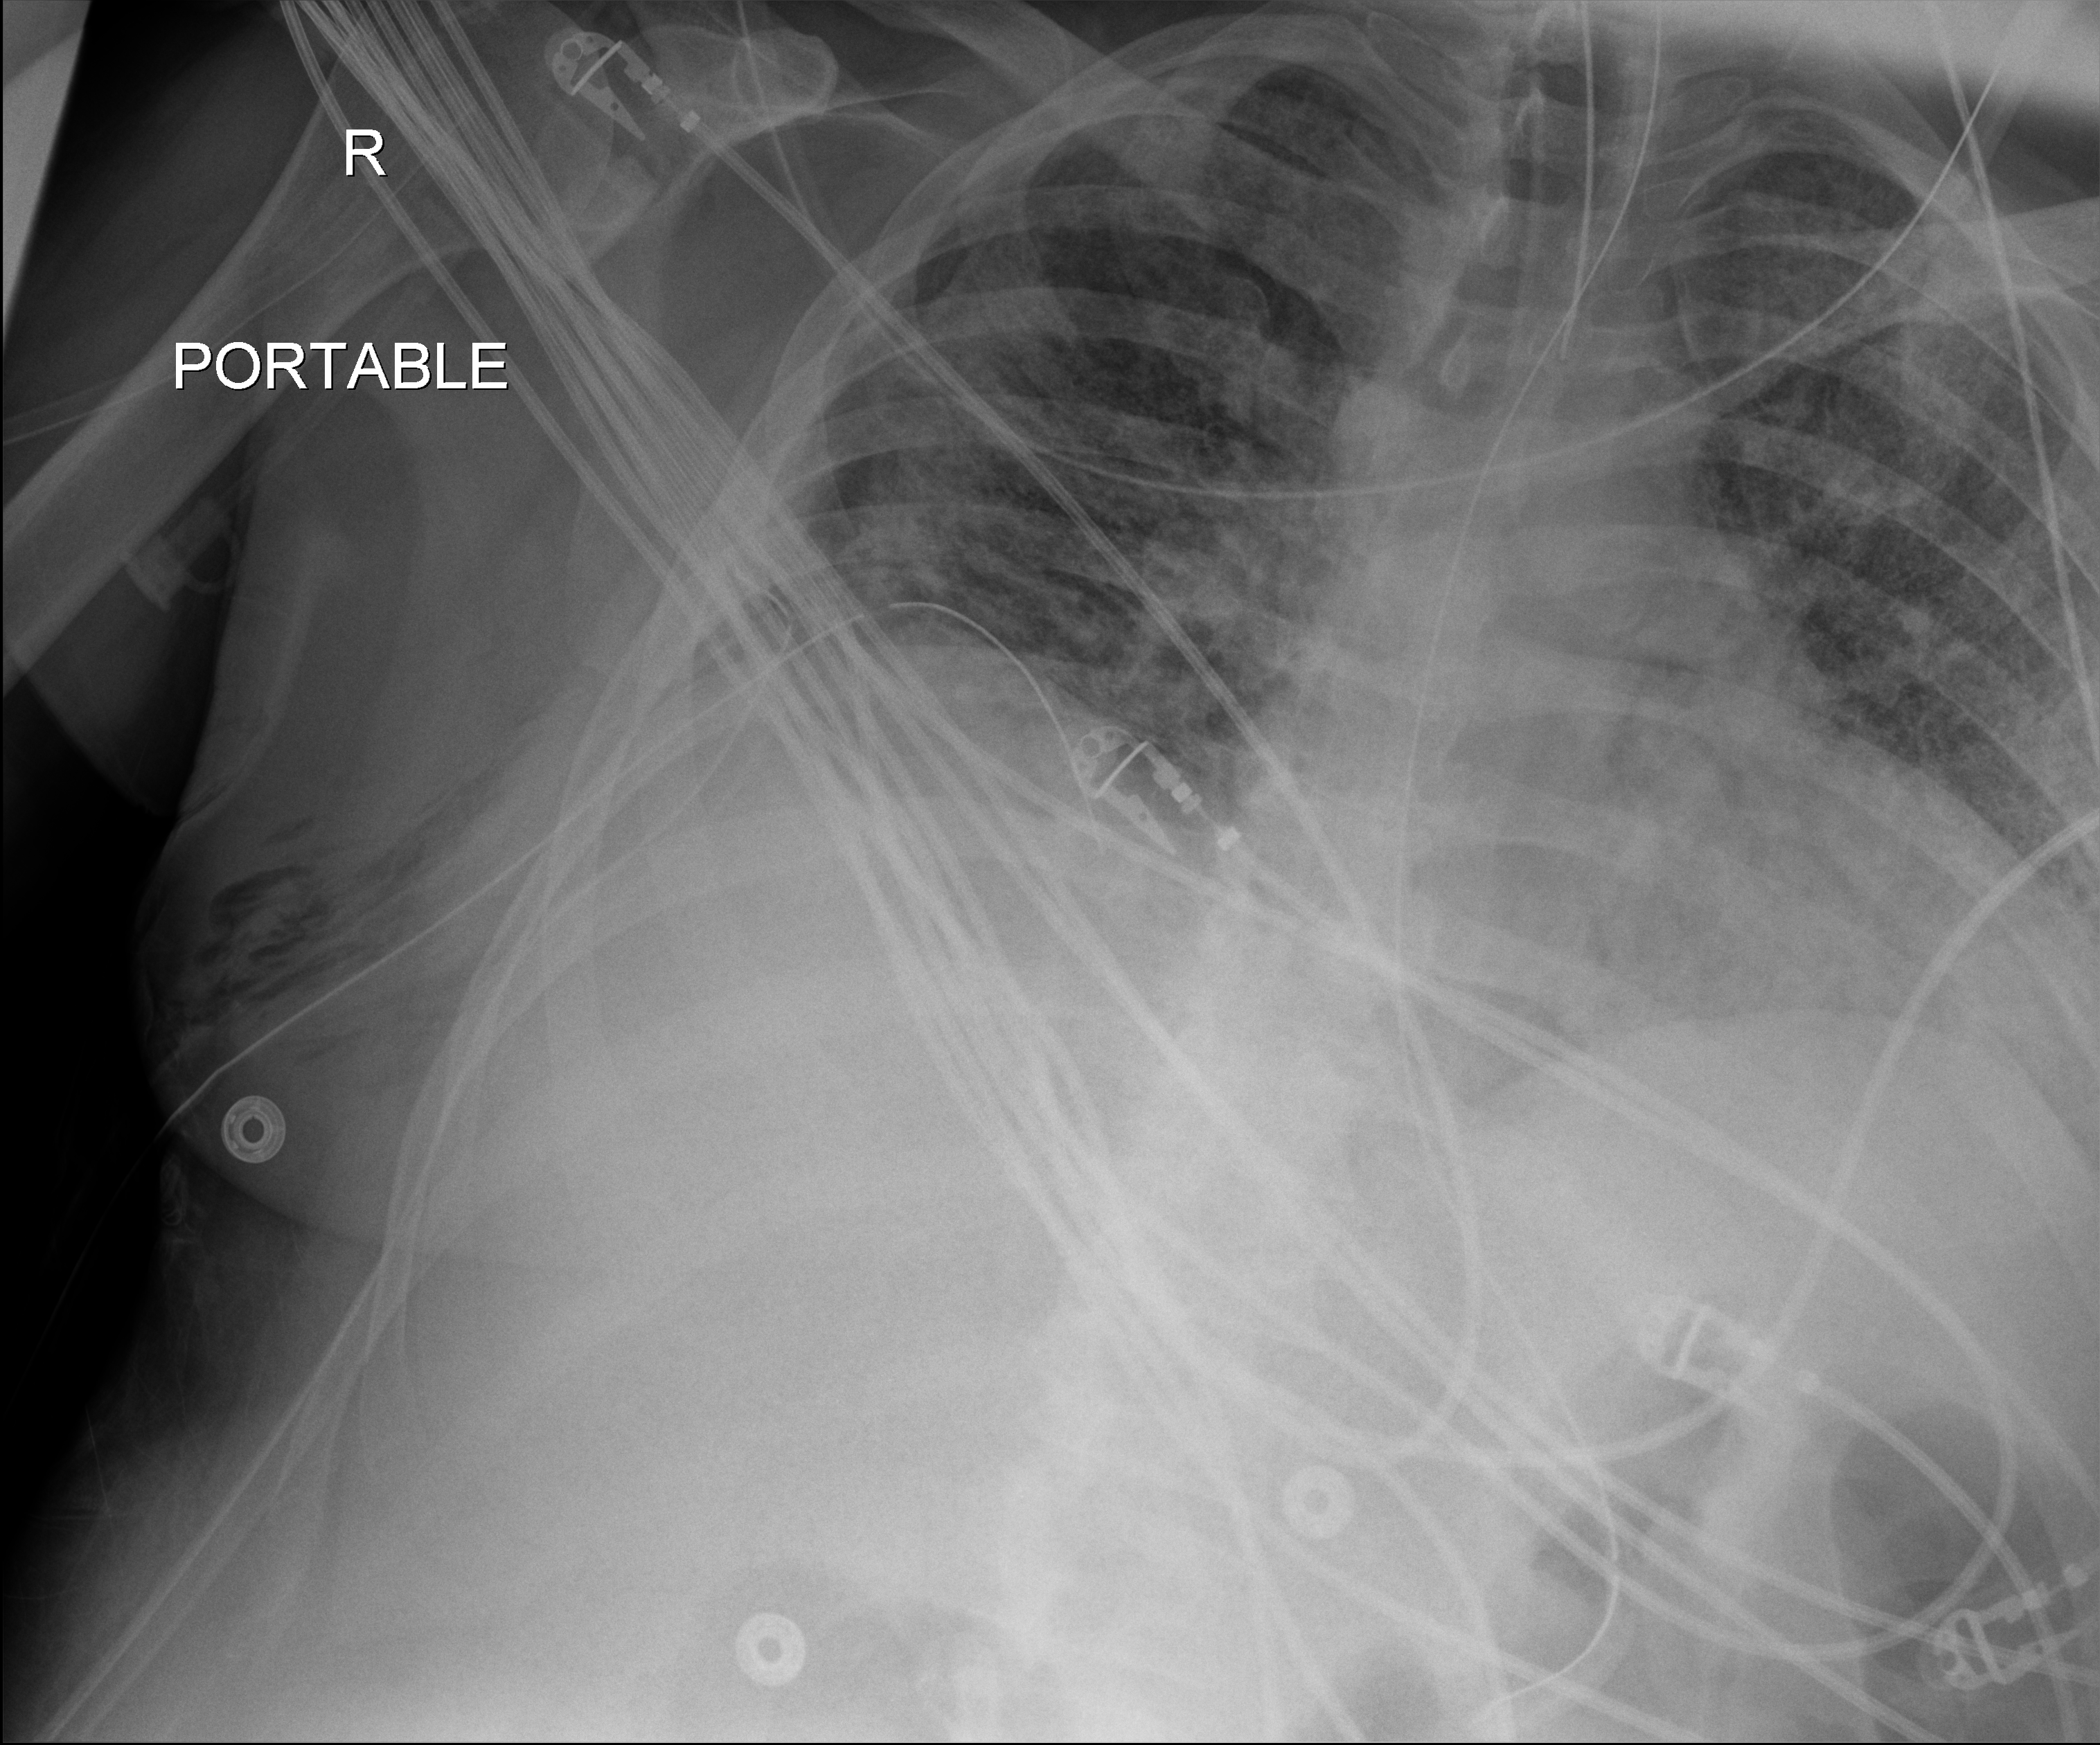
Portable chest radiograph, anteroposterior (AP) projection. Male patient hospitalised with COVID-19, age 18–59 years.
Hospital-stay facts (about this admission, not read from this image; timing relative to this image not recorded):
- mechanically ventilated during this hospital stay: yes
- admitted to intensive care during this hospital stay: yes